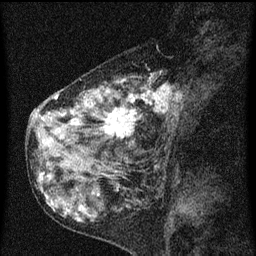
Breast MRI (dynamic contrast-enhanced), one sagittal slice. Position 26 of 60 along the scan axis. Dynamic contrast-enhanced series, image 2 of 3 at this slice position (ordered by acquisition). 1.5 T. TE 4.2 ms, TR 8 ms. 2 mm slice thickness. 256 × 256 image matrix, field of view 180 × 180 mm. Female patient, age 55 years.
Outlined on this slice (semi-automatically segmented with operator editing):
- analysis volume of interest (the breast-tissue region the enhancement analysis was run in; not a lesion): bounding box (x1, y1, x2, y2) in pixels: (42, 72, 185, 155)
- tumour enhancement mask (voxels above the 70 % enhancement threshold inside the analysis volume of interest): (55, 86, 182, 143)